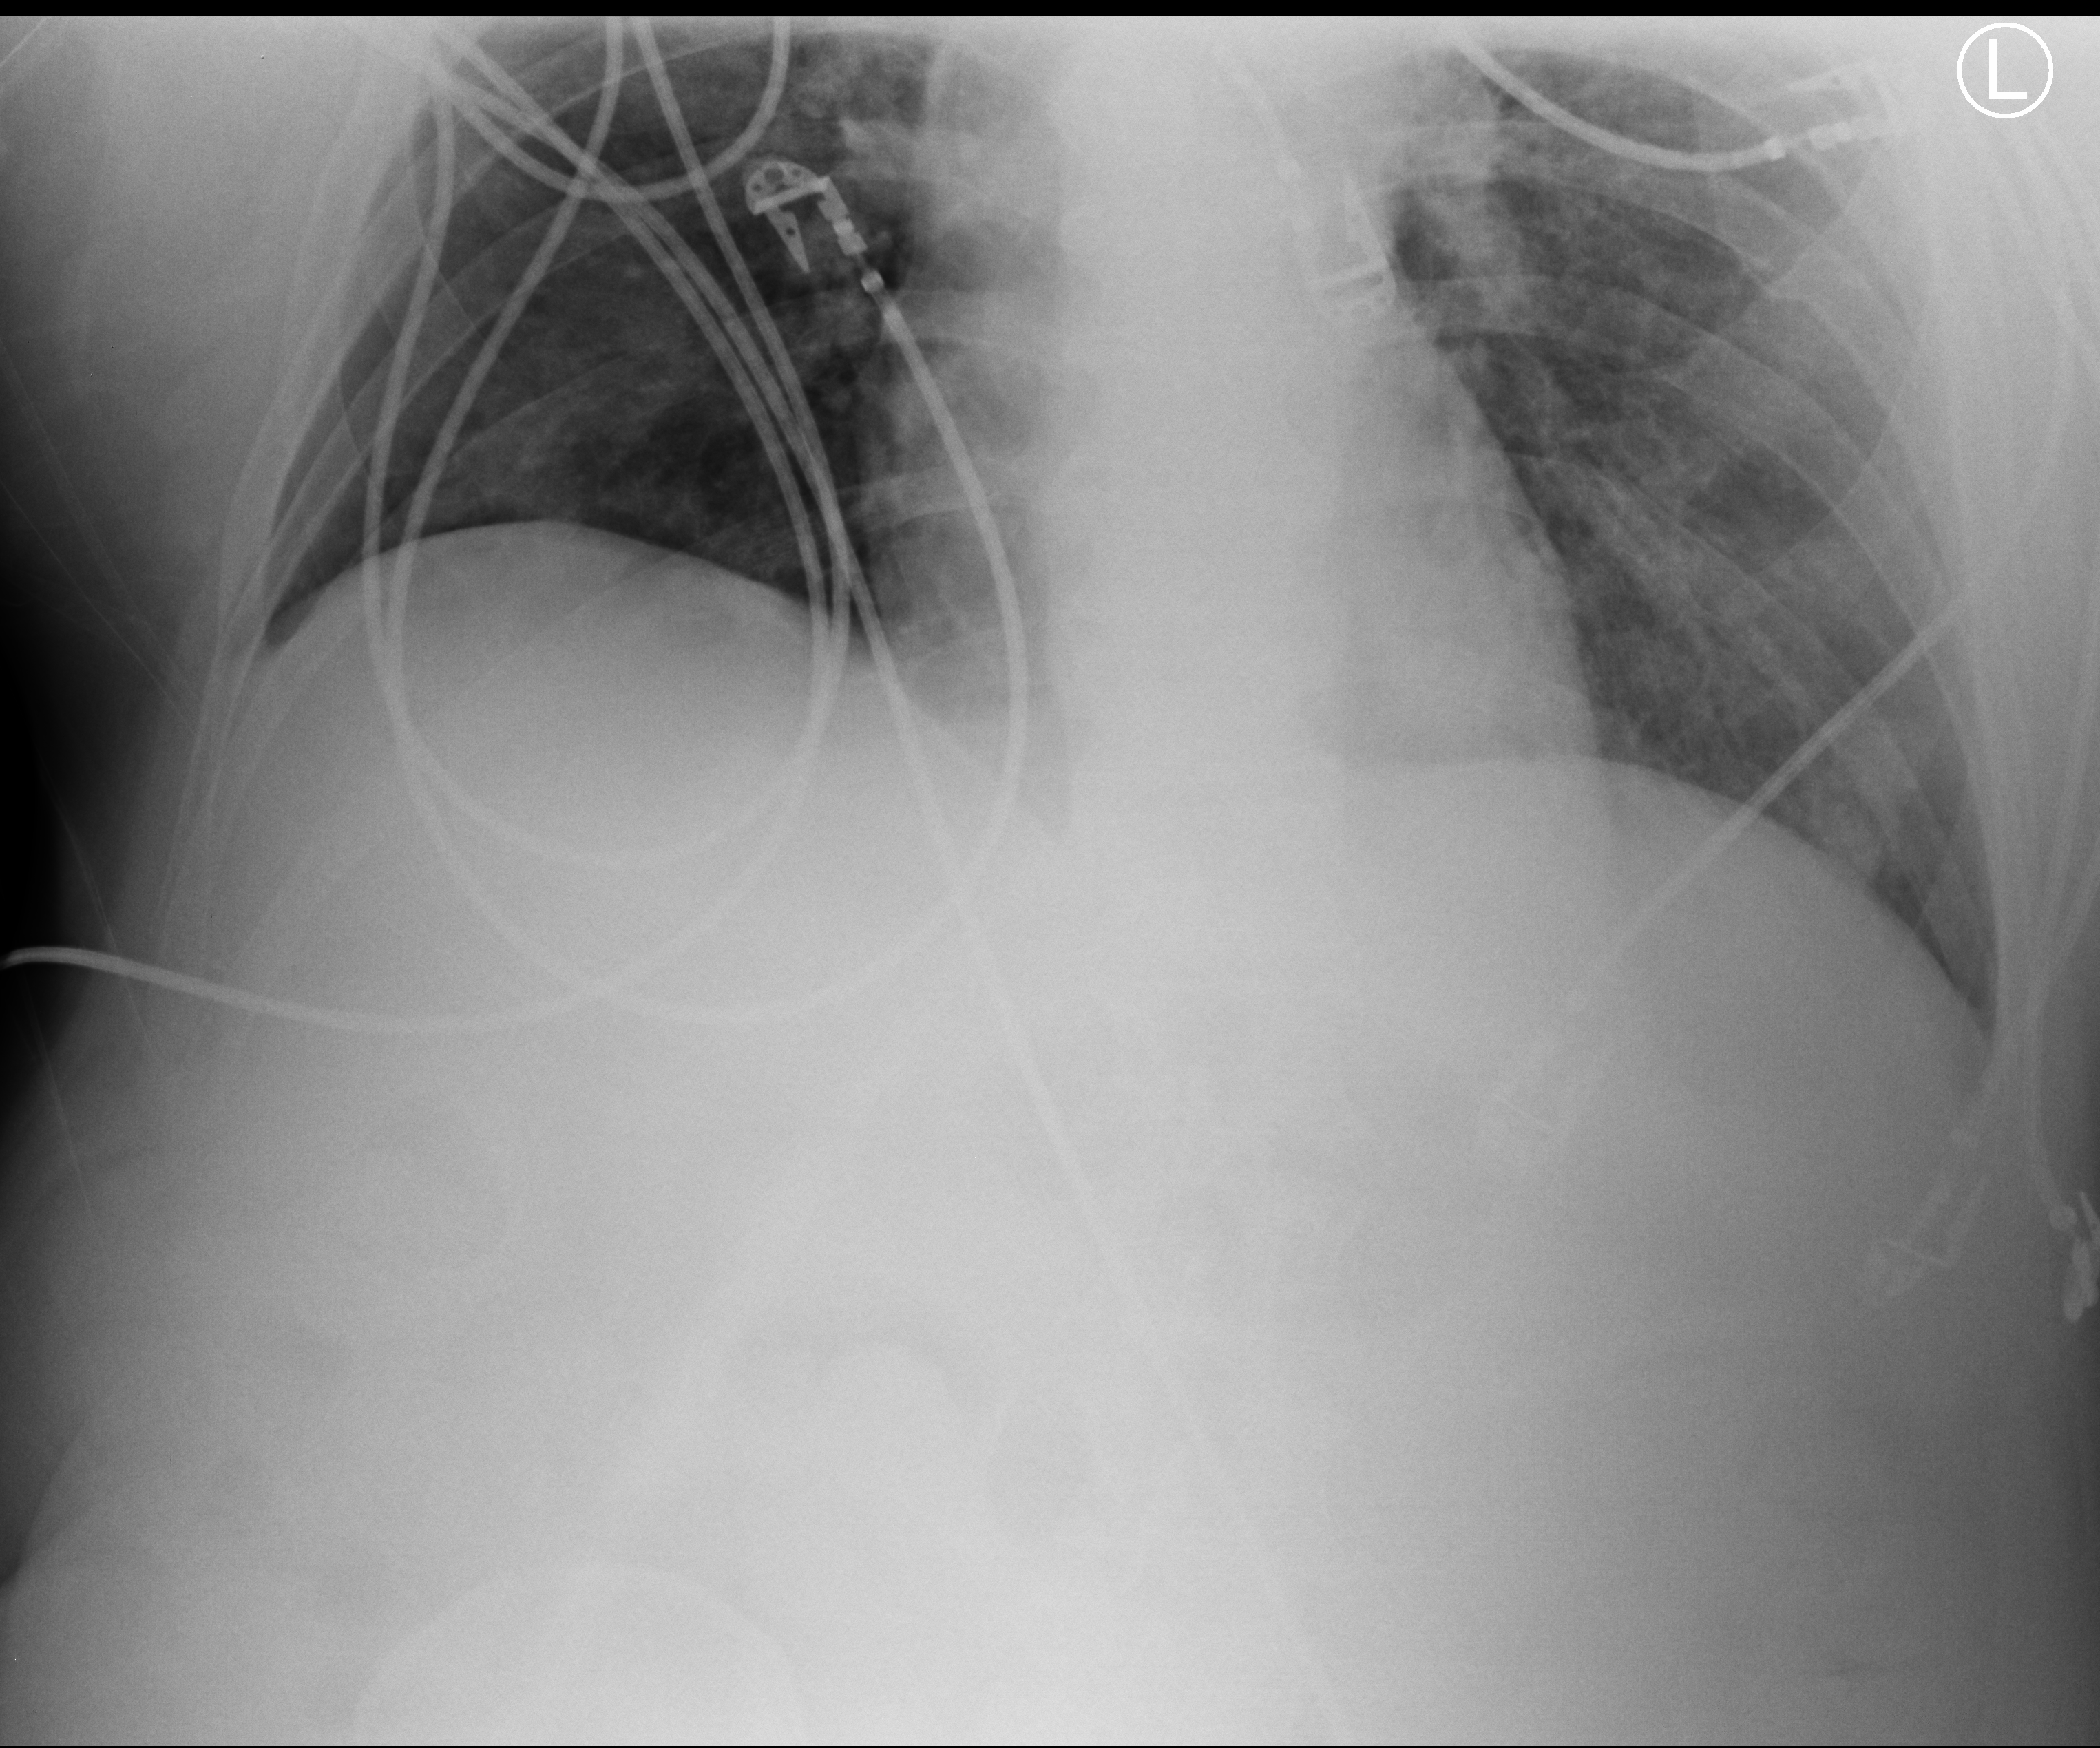
Bedside chest radiograph (computed radiography); anteroposterior (AP) projection. Patient hospitalised with COVID-19, aged 18–59 years.
Admission-level facts for this patient (not findings on this image; timing relative to this image not recorded): admitted to intensive care during this hospital stay: yes.